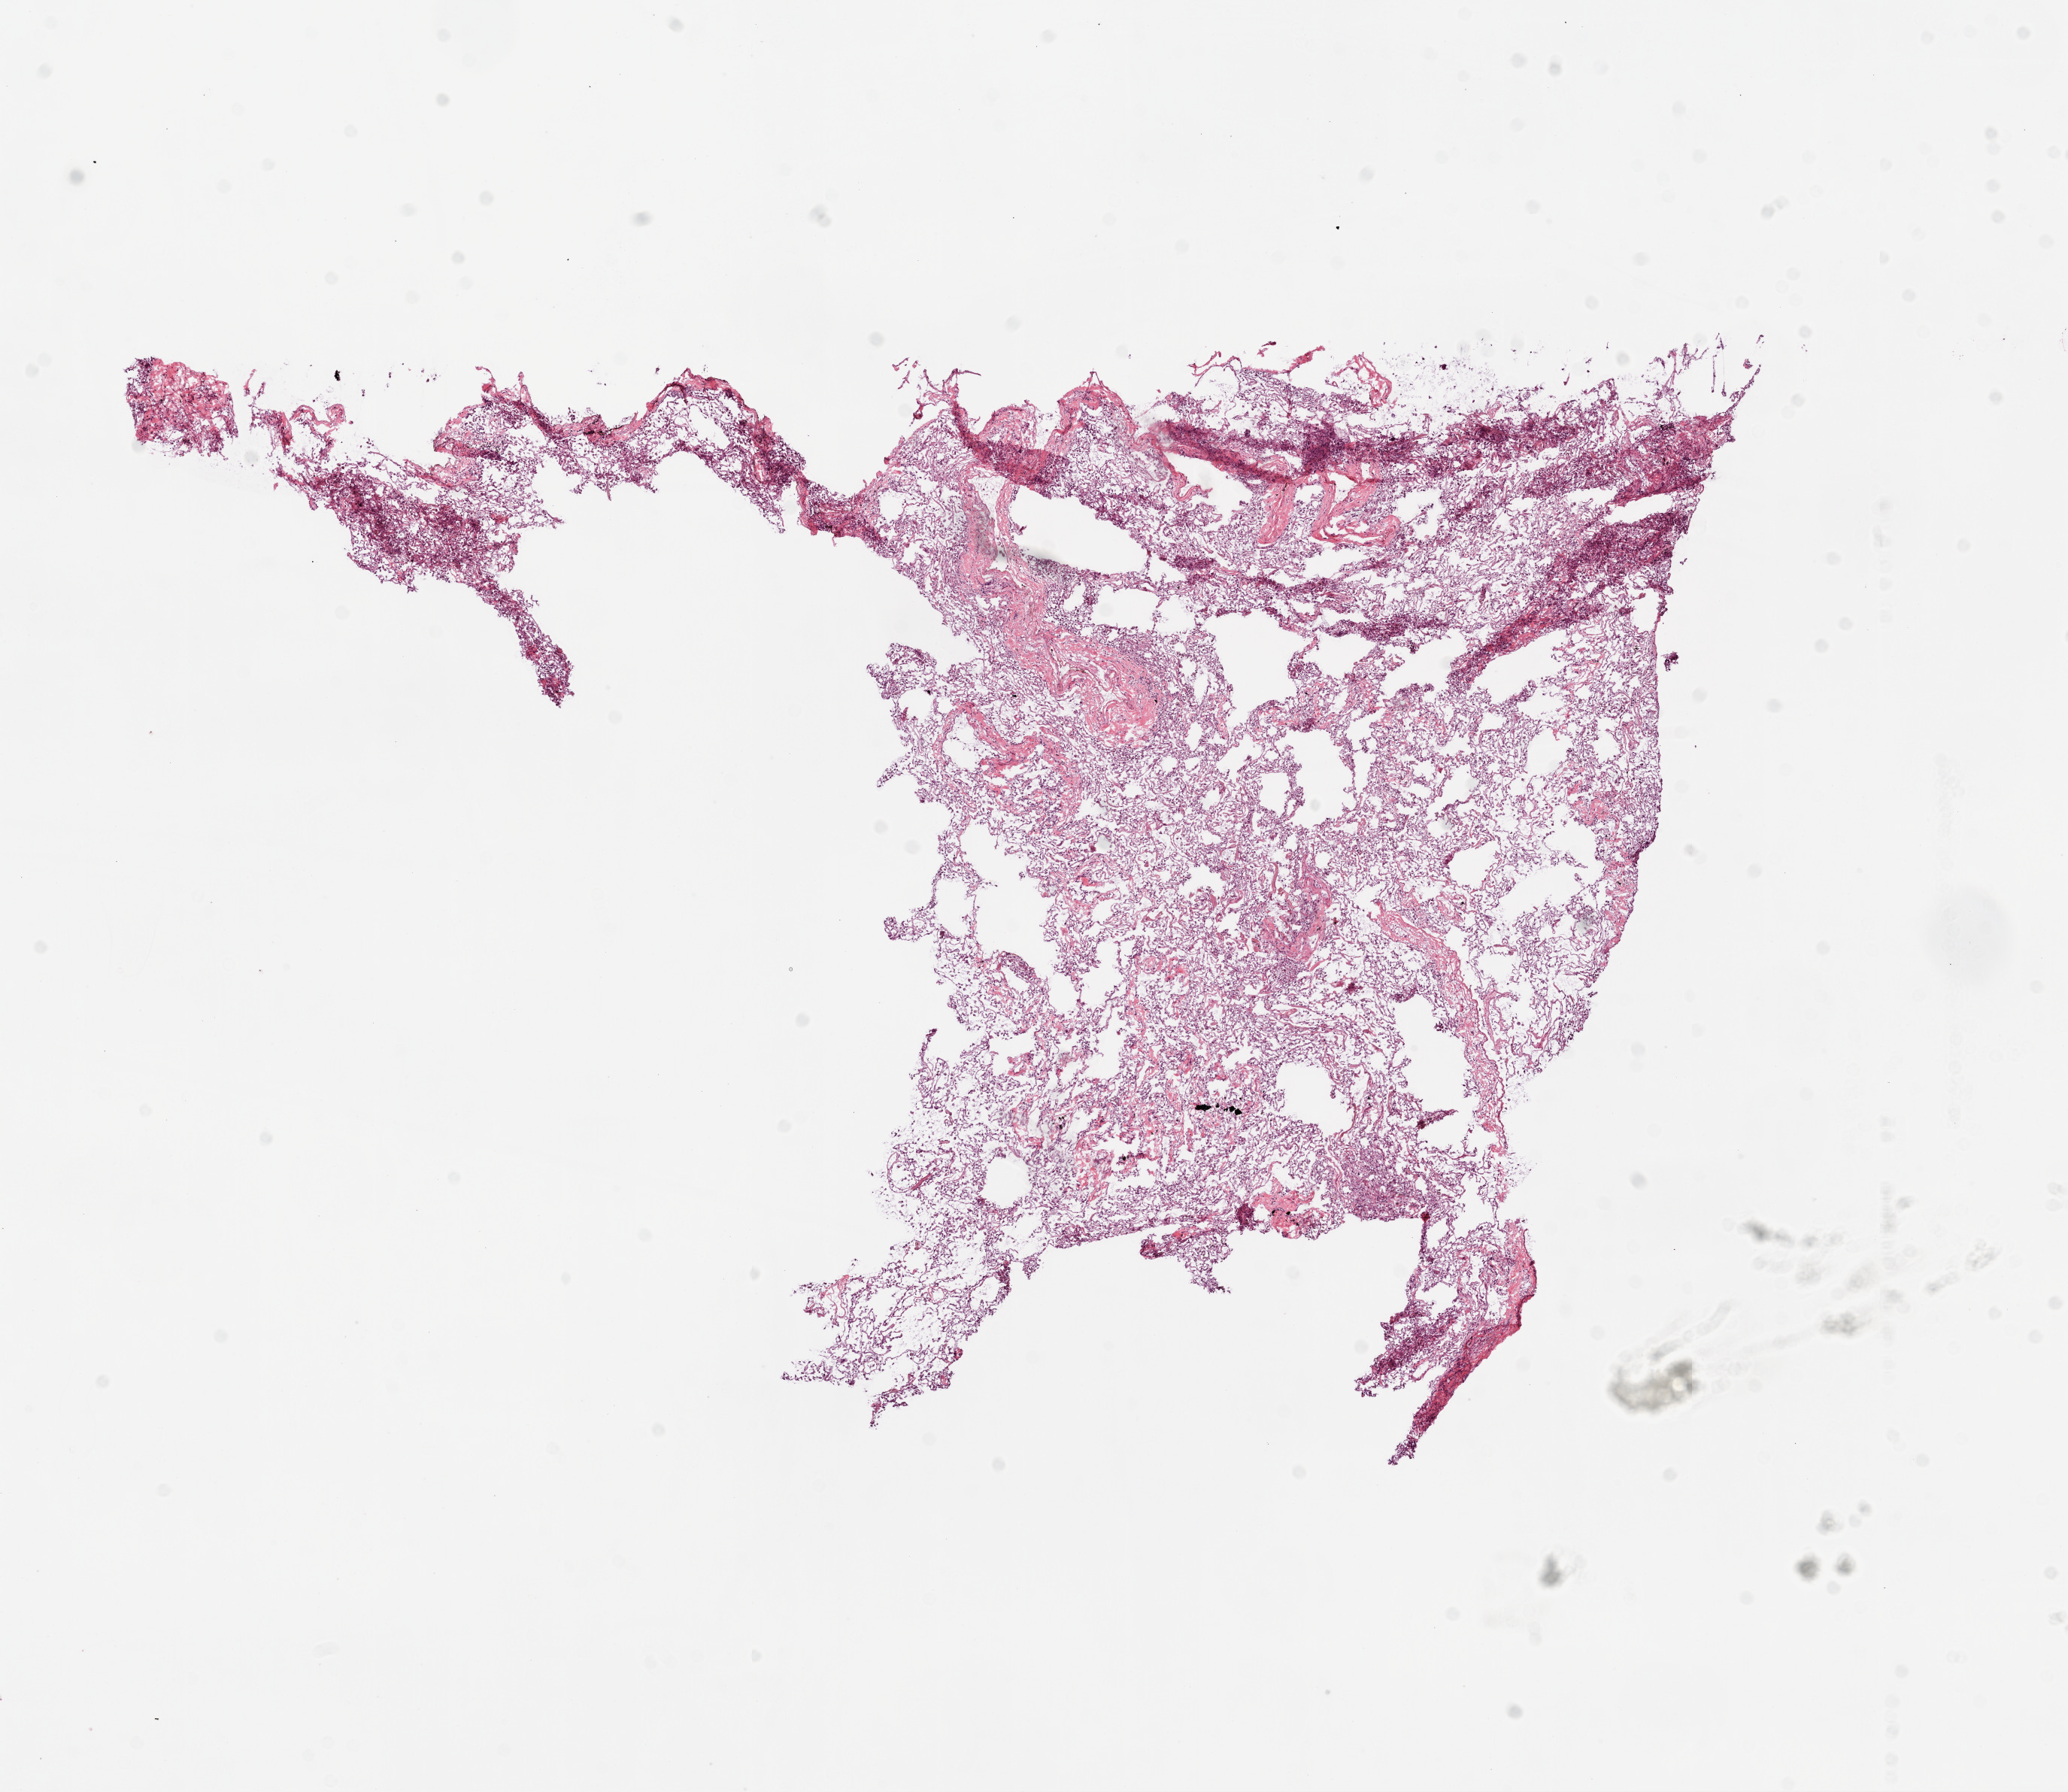
Hematoxylin and eosin (H&E) stained whole-slide image — whole scanned area (about 11.0 x 9.6 mm, slide scanned at 20x) shown as a low-resolution overview, frozen section, solid tissue normal (non-tumour tissue) sample from the lung. Male, age 59 years at initial diagnosis.
This section: solid tissue normal (non-tumour) sample from the same patient. Patient diagnosis: Adenocarcinoma, NOS (lower lobe, lung).